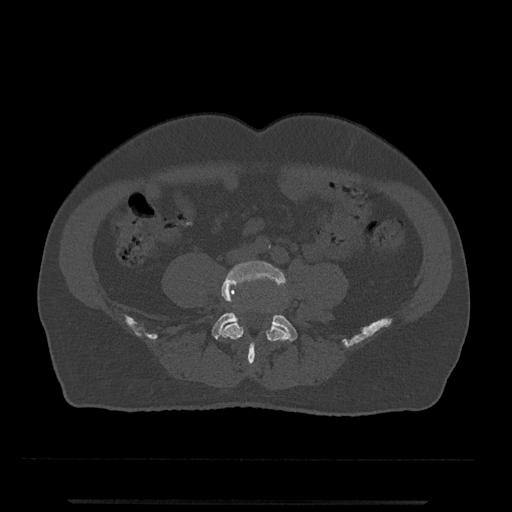
CT including the spine, one axial slice. Position 104 of 797 along the scan axis. Reconstruction kernel Br40s/3. Bone window (W 1800 / L 400 HU). 0.5 mm slice thickness. 512 × 512 image matrix, field of view 419 × 419 mm. Patient: male, 63 years. Case-level facts recorded for this patient, not image findings: primary cancer: prostate.
Structures marked on this image (semi-automatic segmentation, software-assisted and operator-edited):
- L4 vertebra: box from (x=220, y=261) to (x=291, y=366) px
- L5 vertebra: (x=212, y=313)–(x=298, y=359)